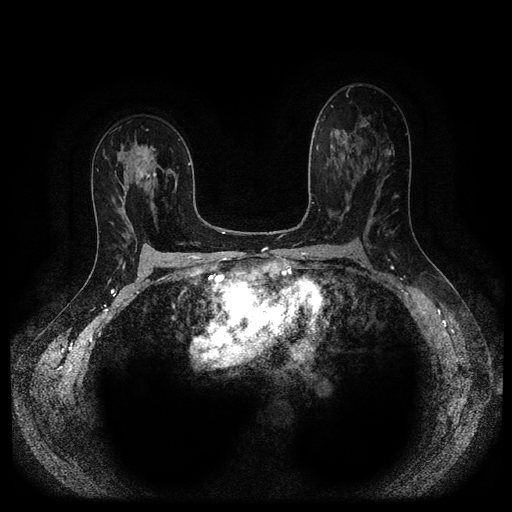
Breast MRI (dynamic contrast-enhanced, multi-phase), one axial slice; position 59 of 116 along the scan axis; dynamic contrast-enhanced series, time point 2 of 5 at this slice position (early post-contrast); 1.5 T; TE 2.6 ms, TR 5.3 ms; 512 × 512 image matrix, field of view 340 × 340 mm. Patient: female, 50 years.
Structures marked on this image (semi-automatically segmented with operator editing):
- breast lesion (labelled 'tumour' in the annotation; benign lesions carry a separate 'benign' label): bounding box (x1, y1, x2, y2) in pixels: (130, 144, 161, 185)